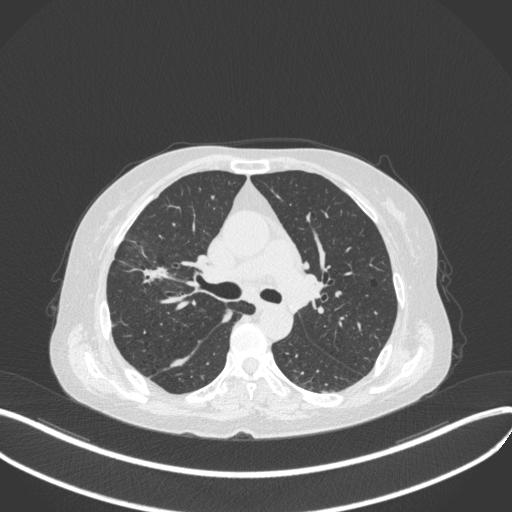
Chest CT, one axial slice. Slice 253 of 429 in the series (ordered by position). Reconstruction kernel B31f. Lung window (W 1500 / L -600 HU). 1 mm slice thickness. 512 × 512 image matrix. Patient: female, 69 years. From the clinical record (not read from this slice): clinical TNM (as recorded): T1b N3 M0.
Outlined on this slice (bounding box drawn by a radiologist):
- lung tumour (recorded histology: small cell carcinoma): bounding box [x1, y1, x2, y2] px = [130, 259, 176, 286]